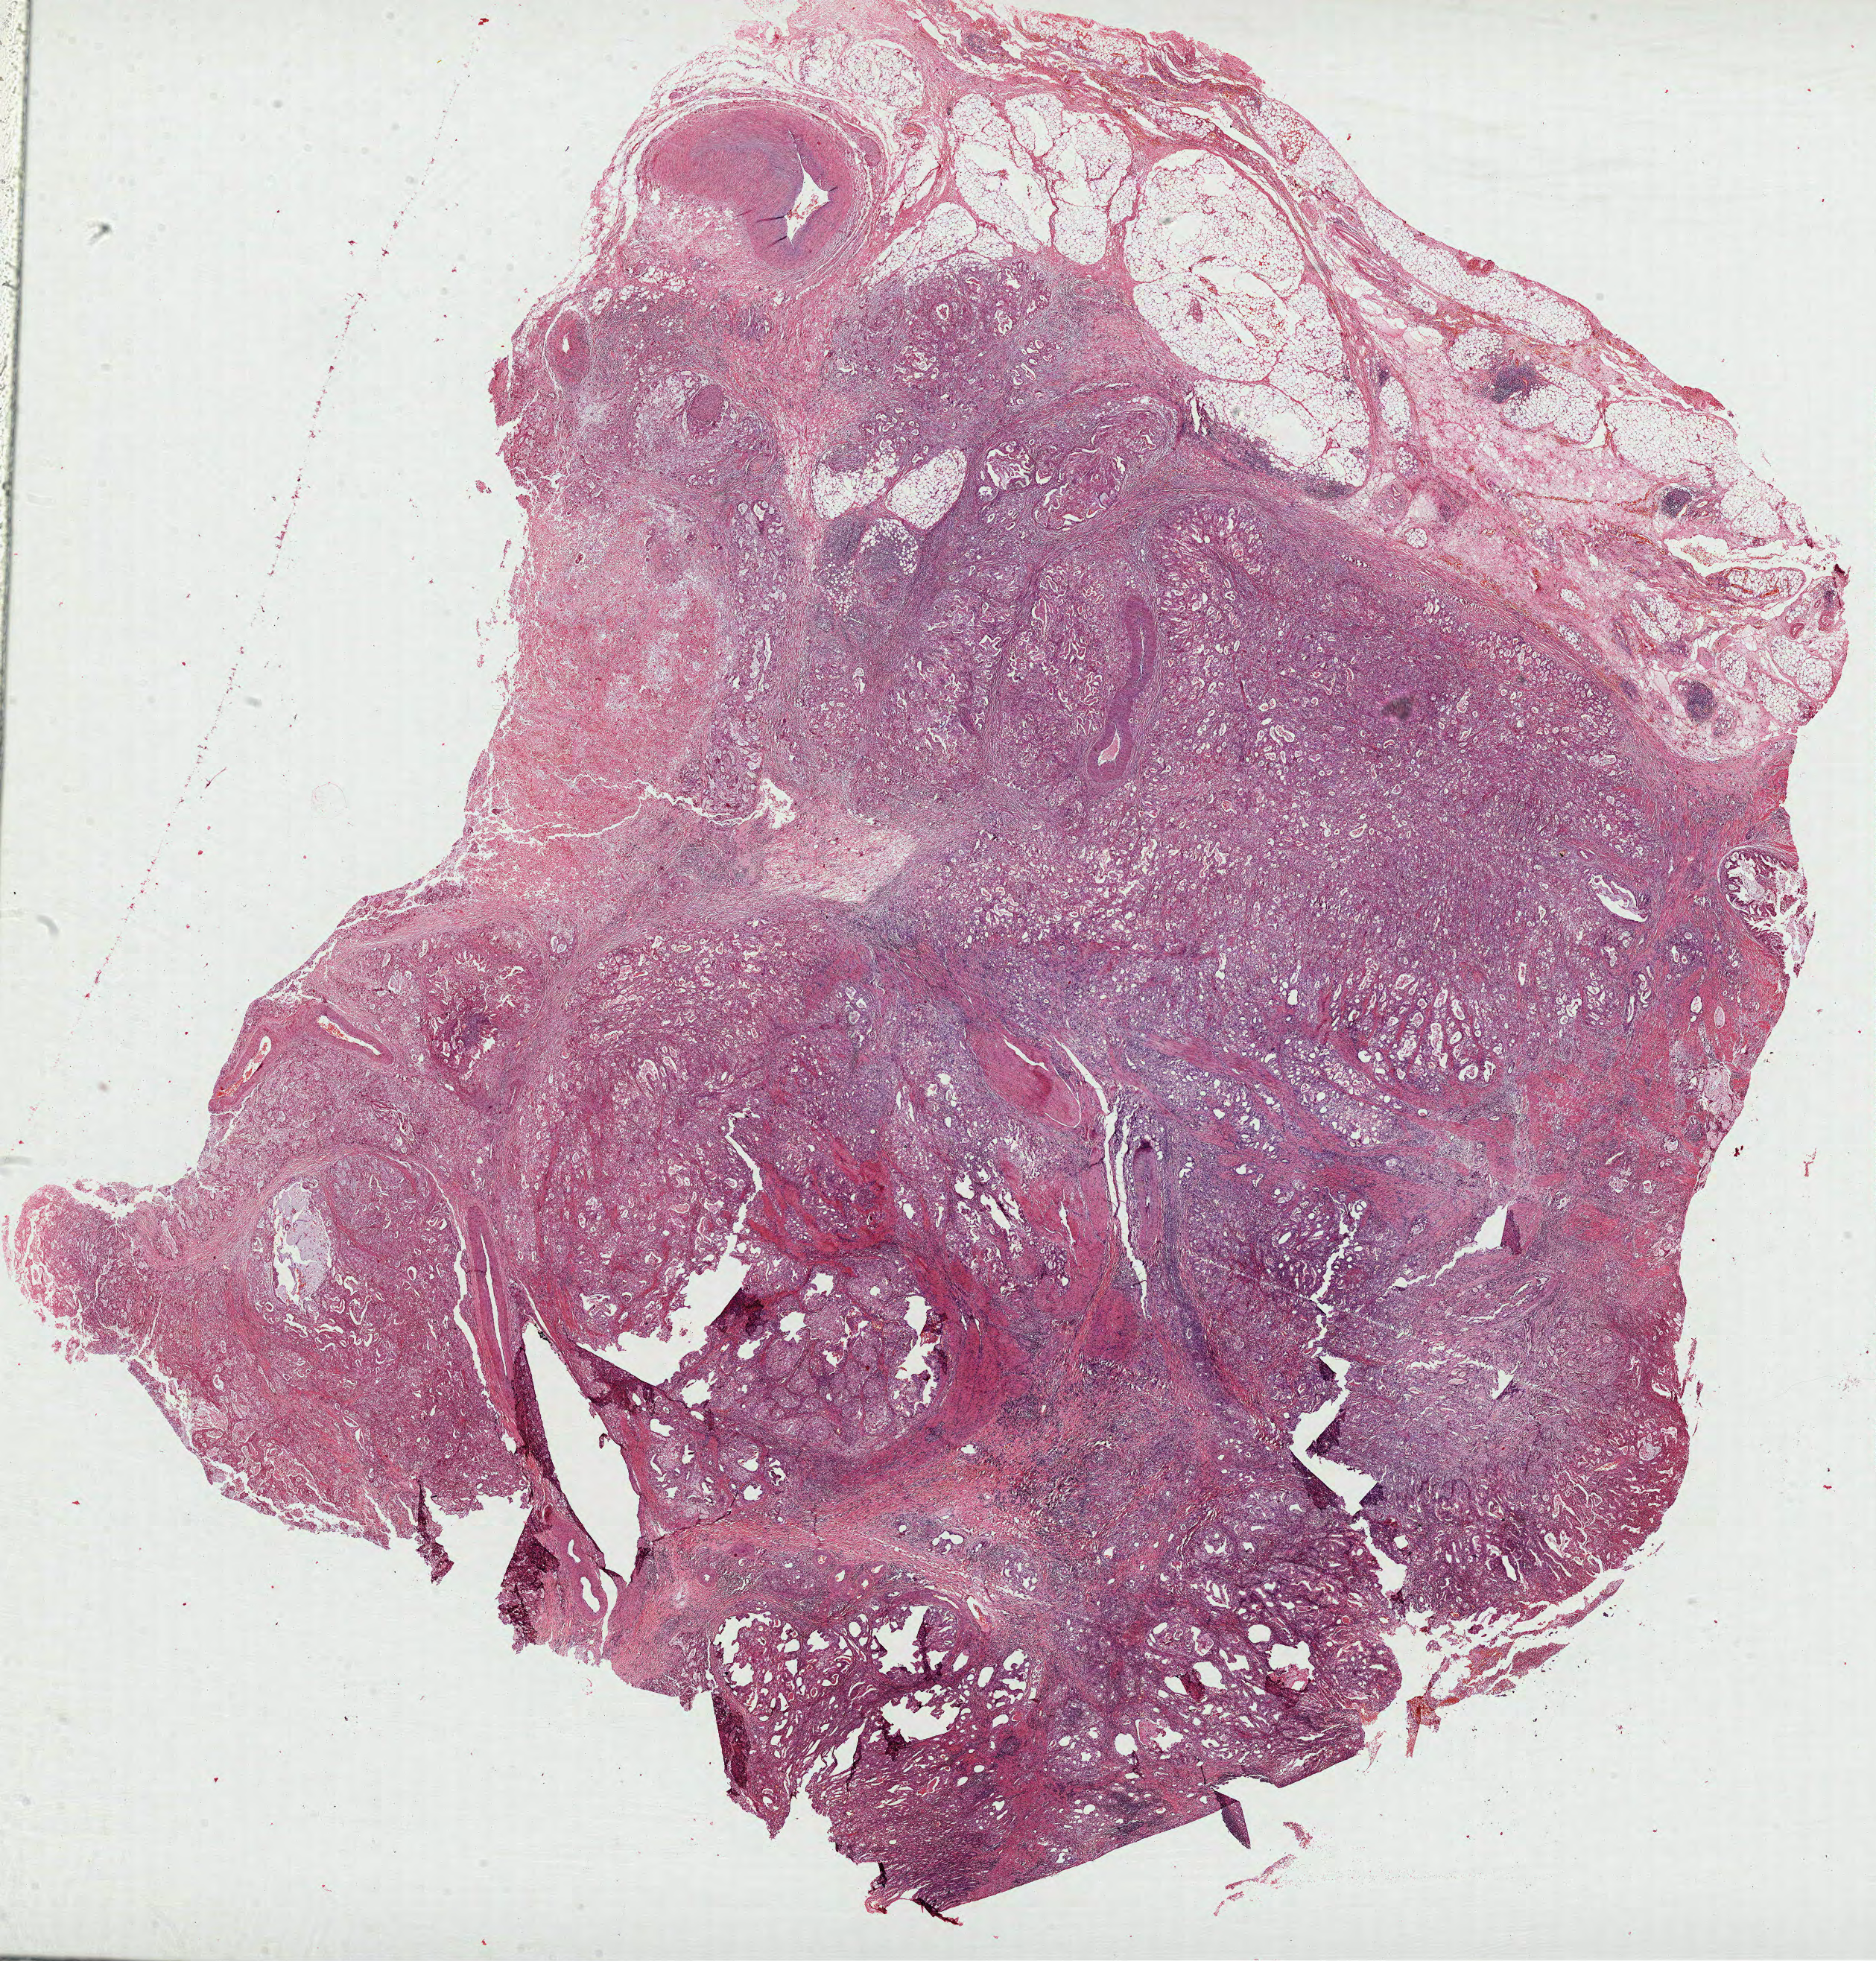
Whole-slide histology image, Hematoxylin and eosin (H&E) stained, shown as a low-resolution overview of the whole scanned area (about 20.3 x 21.2 mm, from a 40x scan); formalin-fixed paraffin-embedded (FFPE) diagnostic section; sample: primary tumour, stomach. Male patient. Histologic grade: G2 (moderately differentiated).
• histologic diagnosis: Adenocarcinoma, NOS (cardia, NOS)